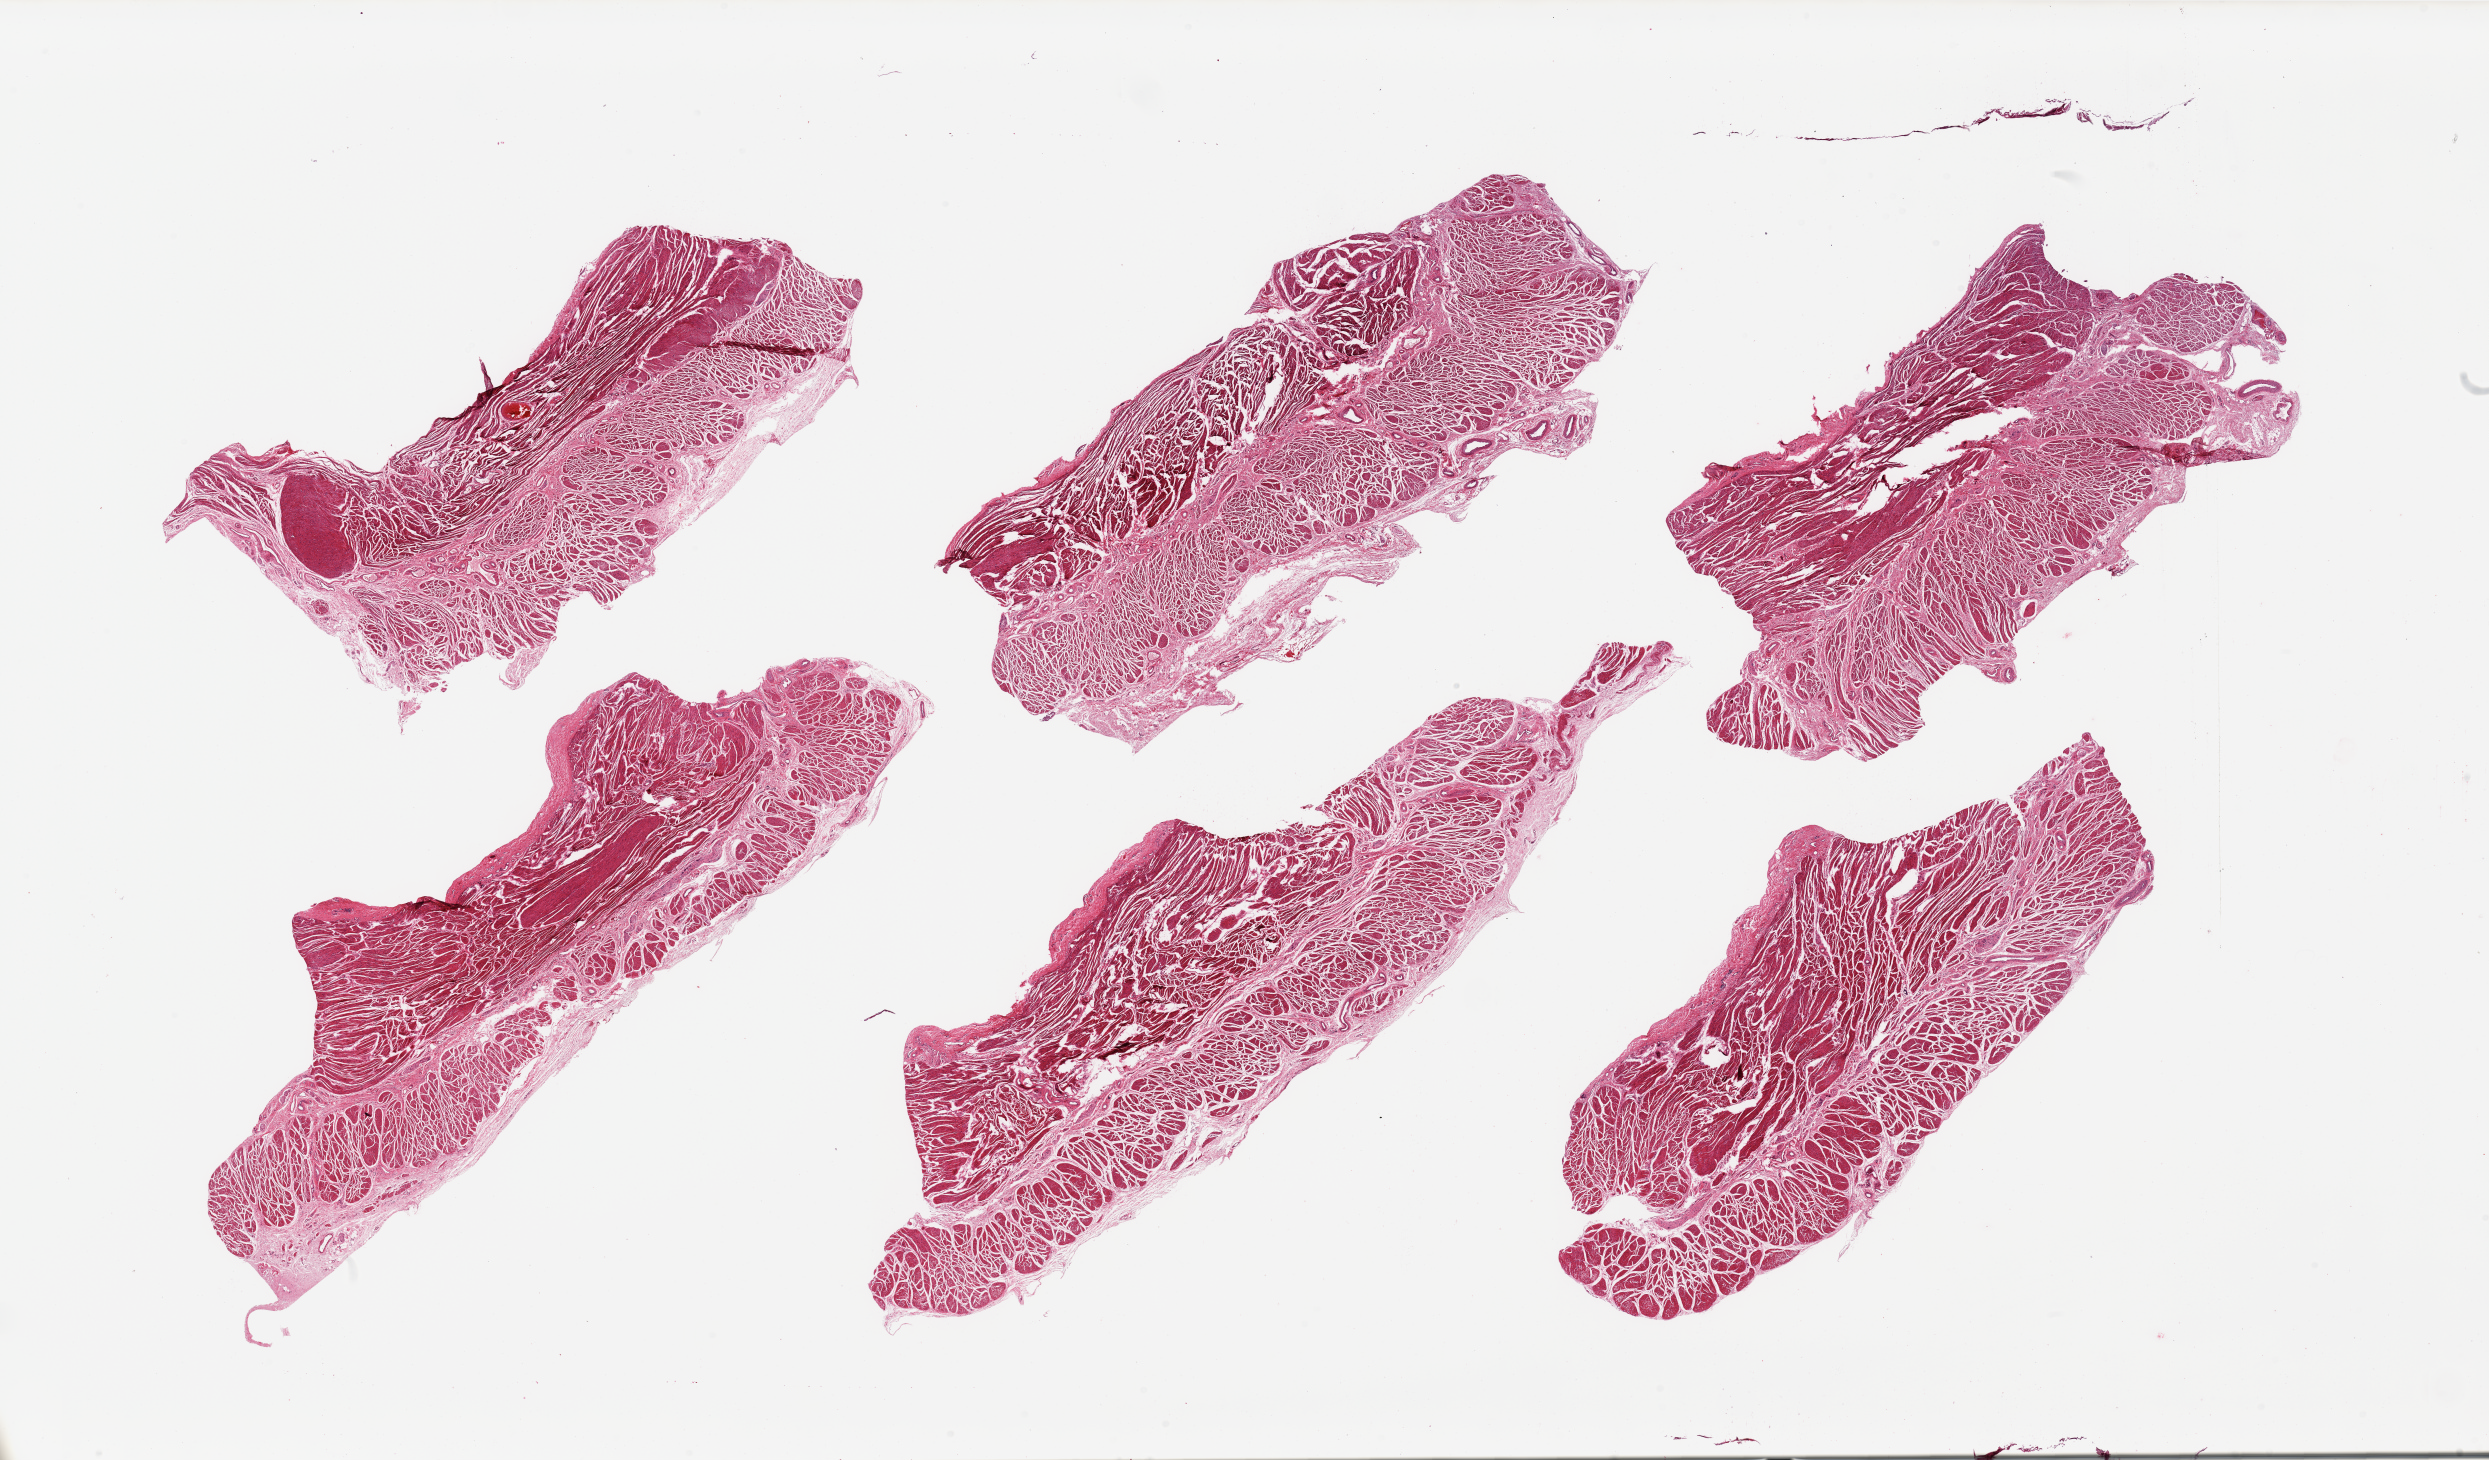
Digitized H&E-stained section, whole scanned area (about 39.4 x 23.1 mm) shown as a low-resolution overview; PAXgene-fixed paraffin-embedded (PFPE) section; target tissue: esophageal muscle; donor tissue sample. Donor: male.
Pathologist's review note for this sample: 6 pieces, confirmed target muscularis.